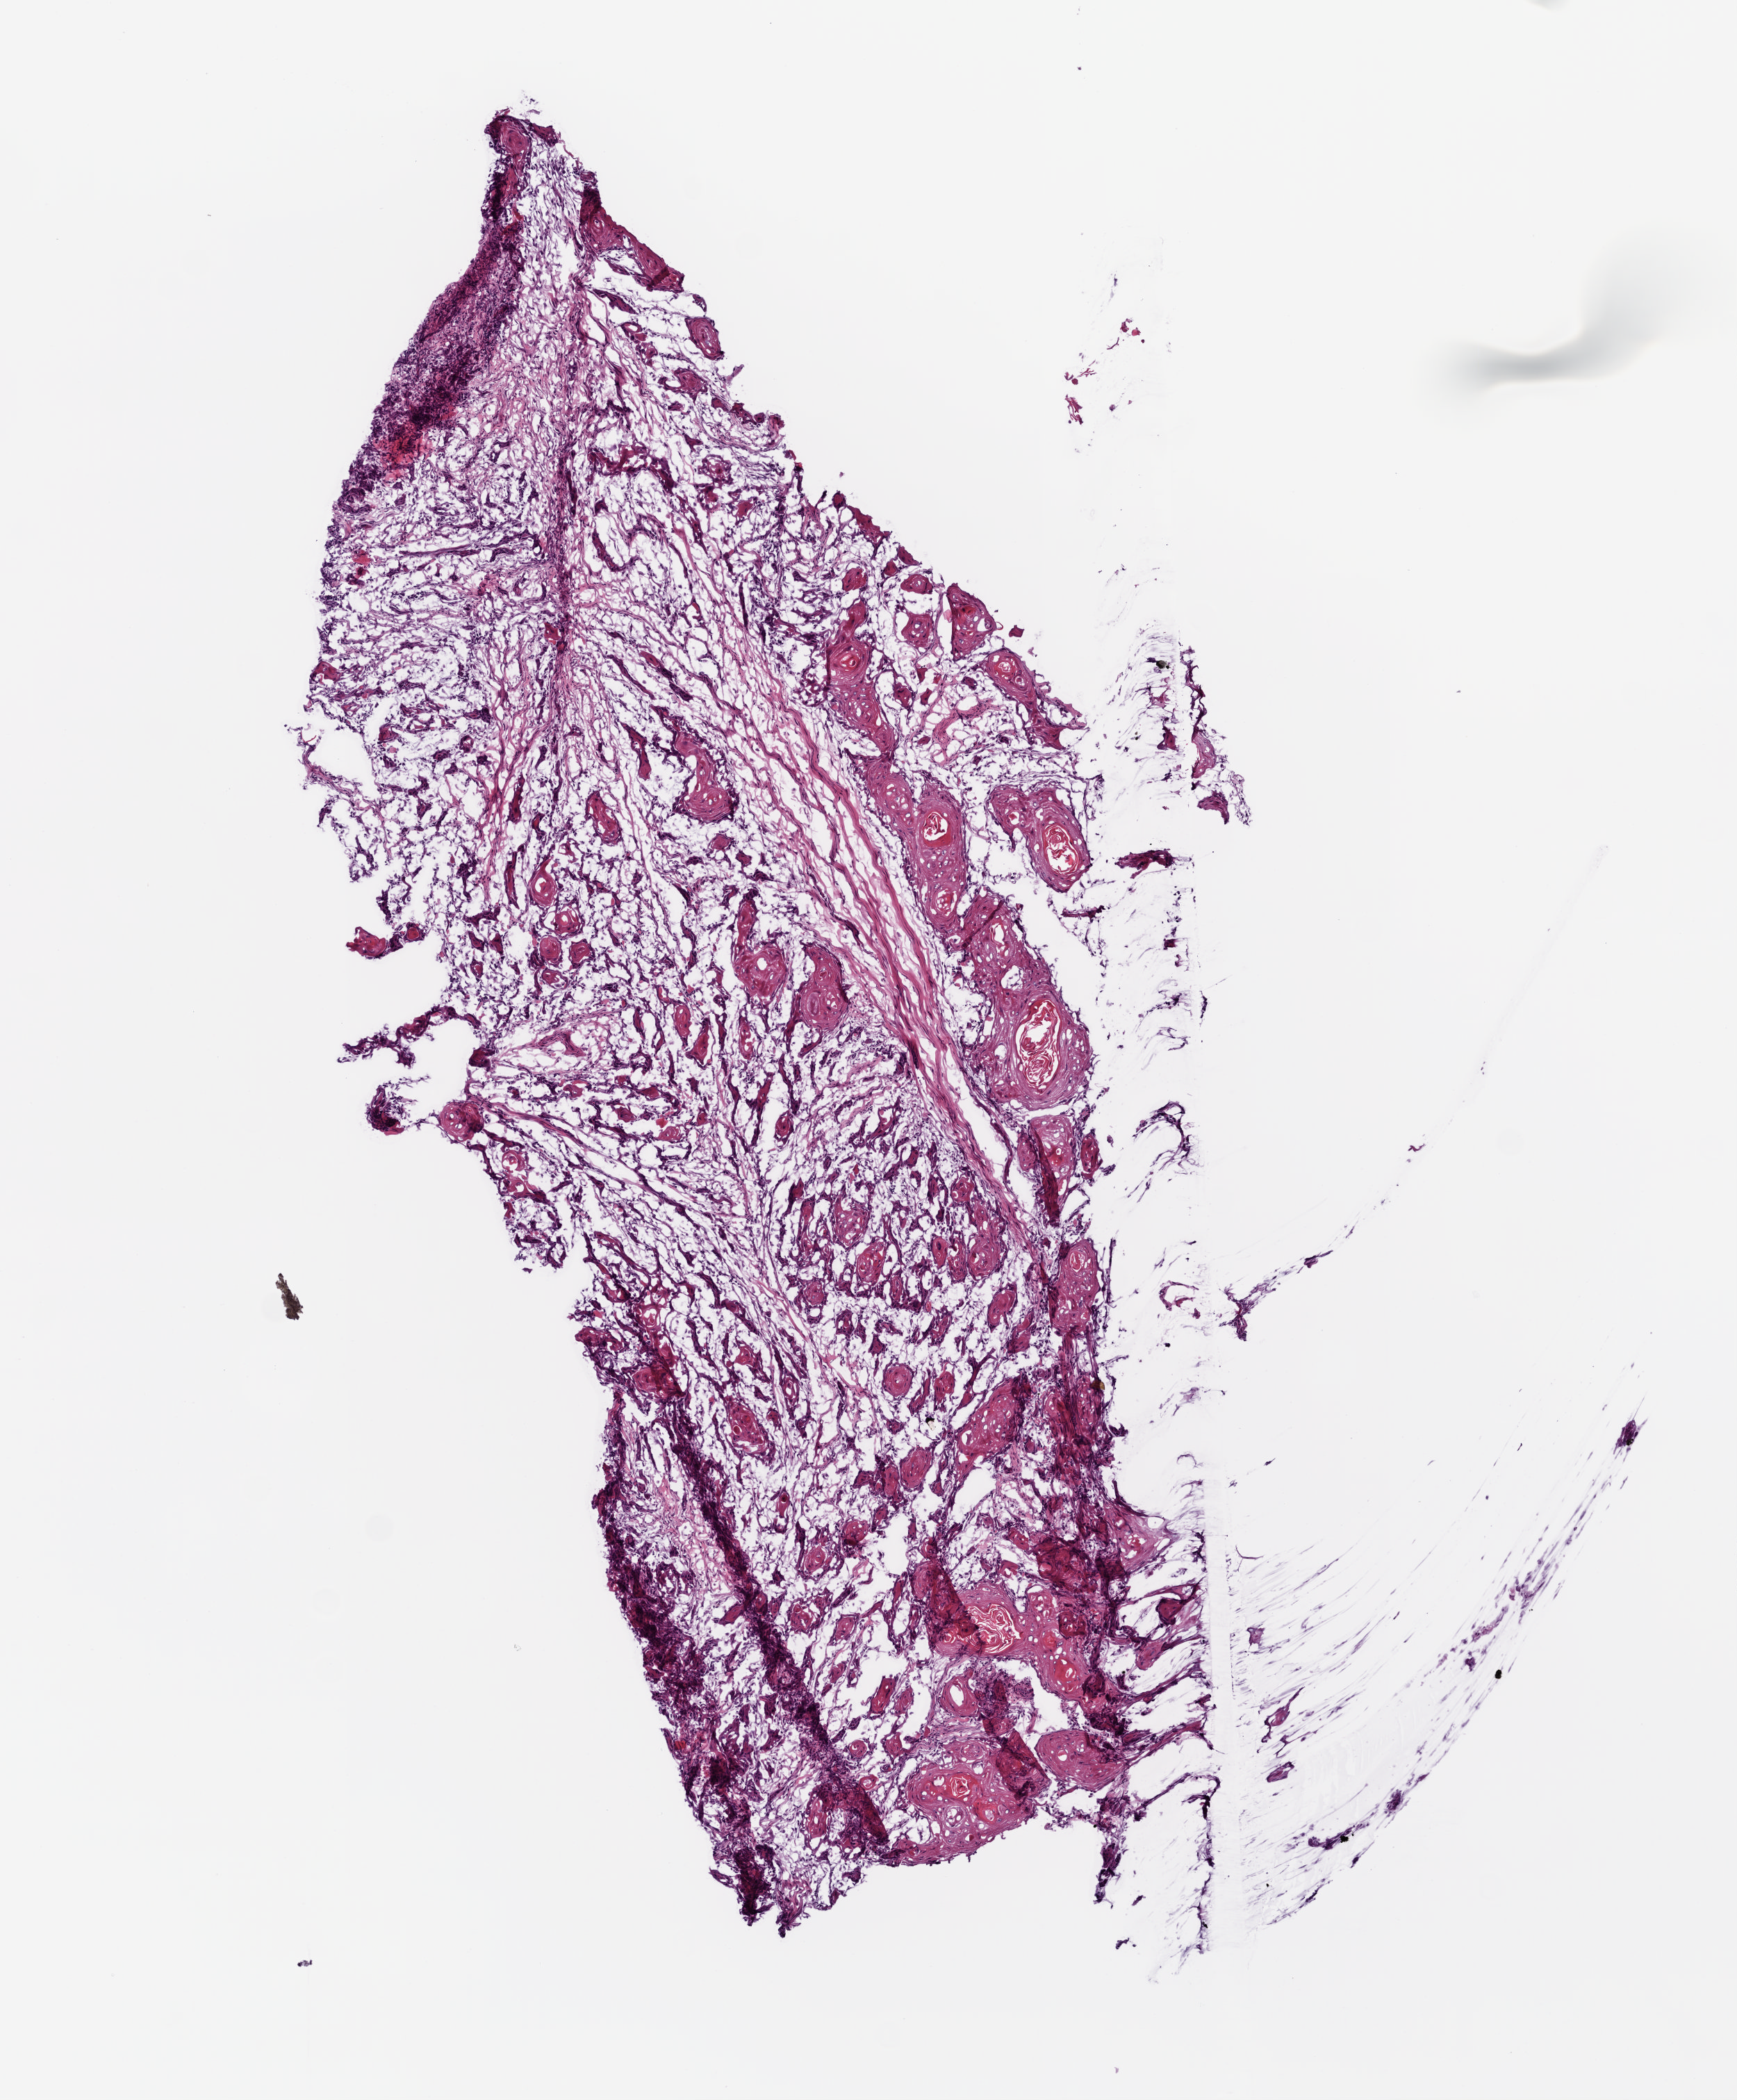
Digitized Hematoxylin and eosin (H&E) stained tissue section (whole slide) — shown as a low-resolution overview of the whole scanned area (about 5.0 x 6.1 mm); frozen section; primary tumour sample from the head and neck. Patient: male, age at initial diagnosis 64 years. Histologic grade: G3 (poorly differentiated). Composition of this section per pathologist review: tumour cells 30%, tumour nuclei 60%, normal cells 0%, stromal cells 70%, necrosis 0%.
* diagnosis: Squamous cell carcinoma, NOS (larynx, NOS)
* AJCC pathologic stage: IVA (7th edition)